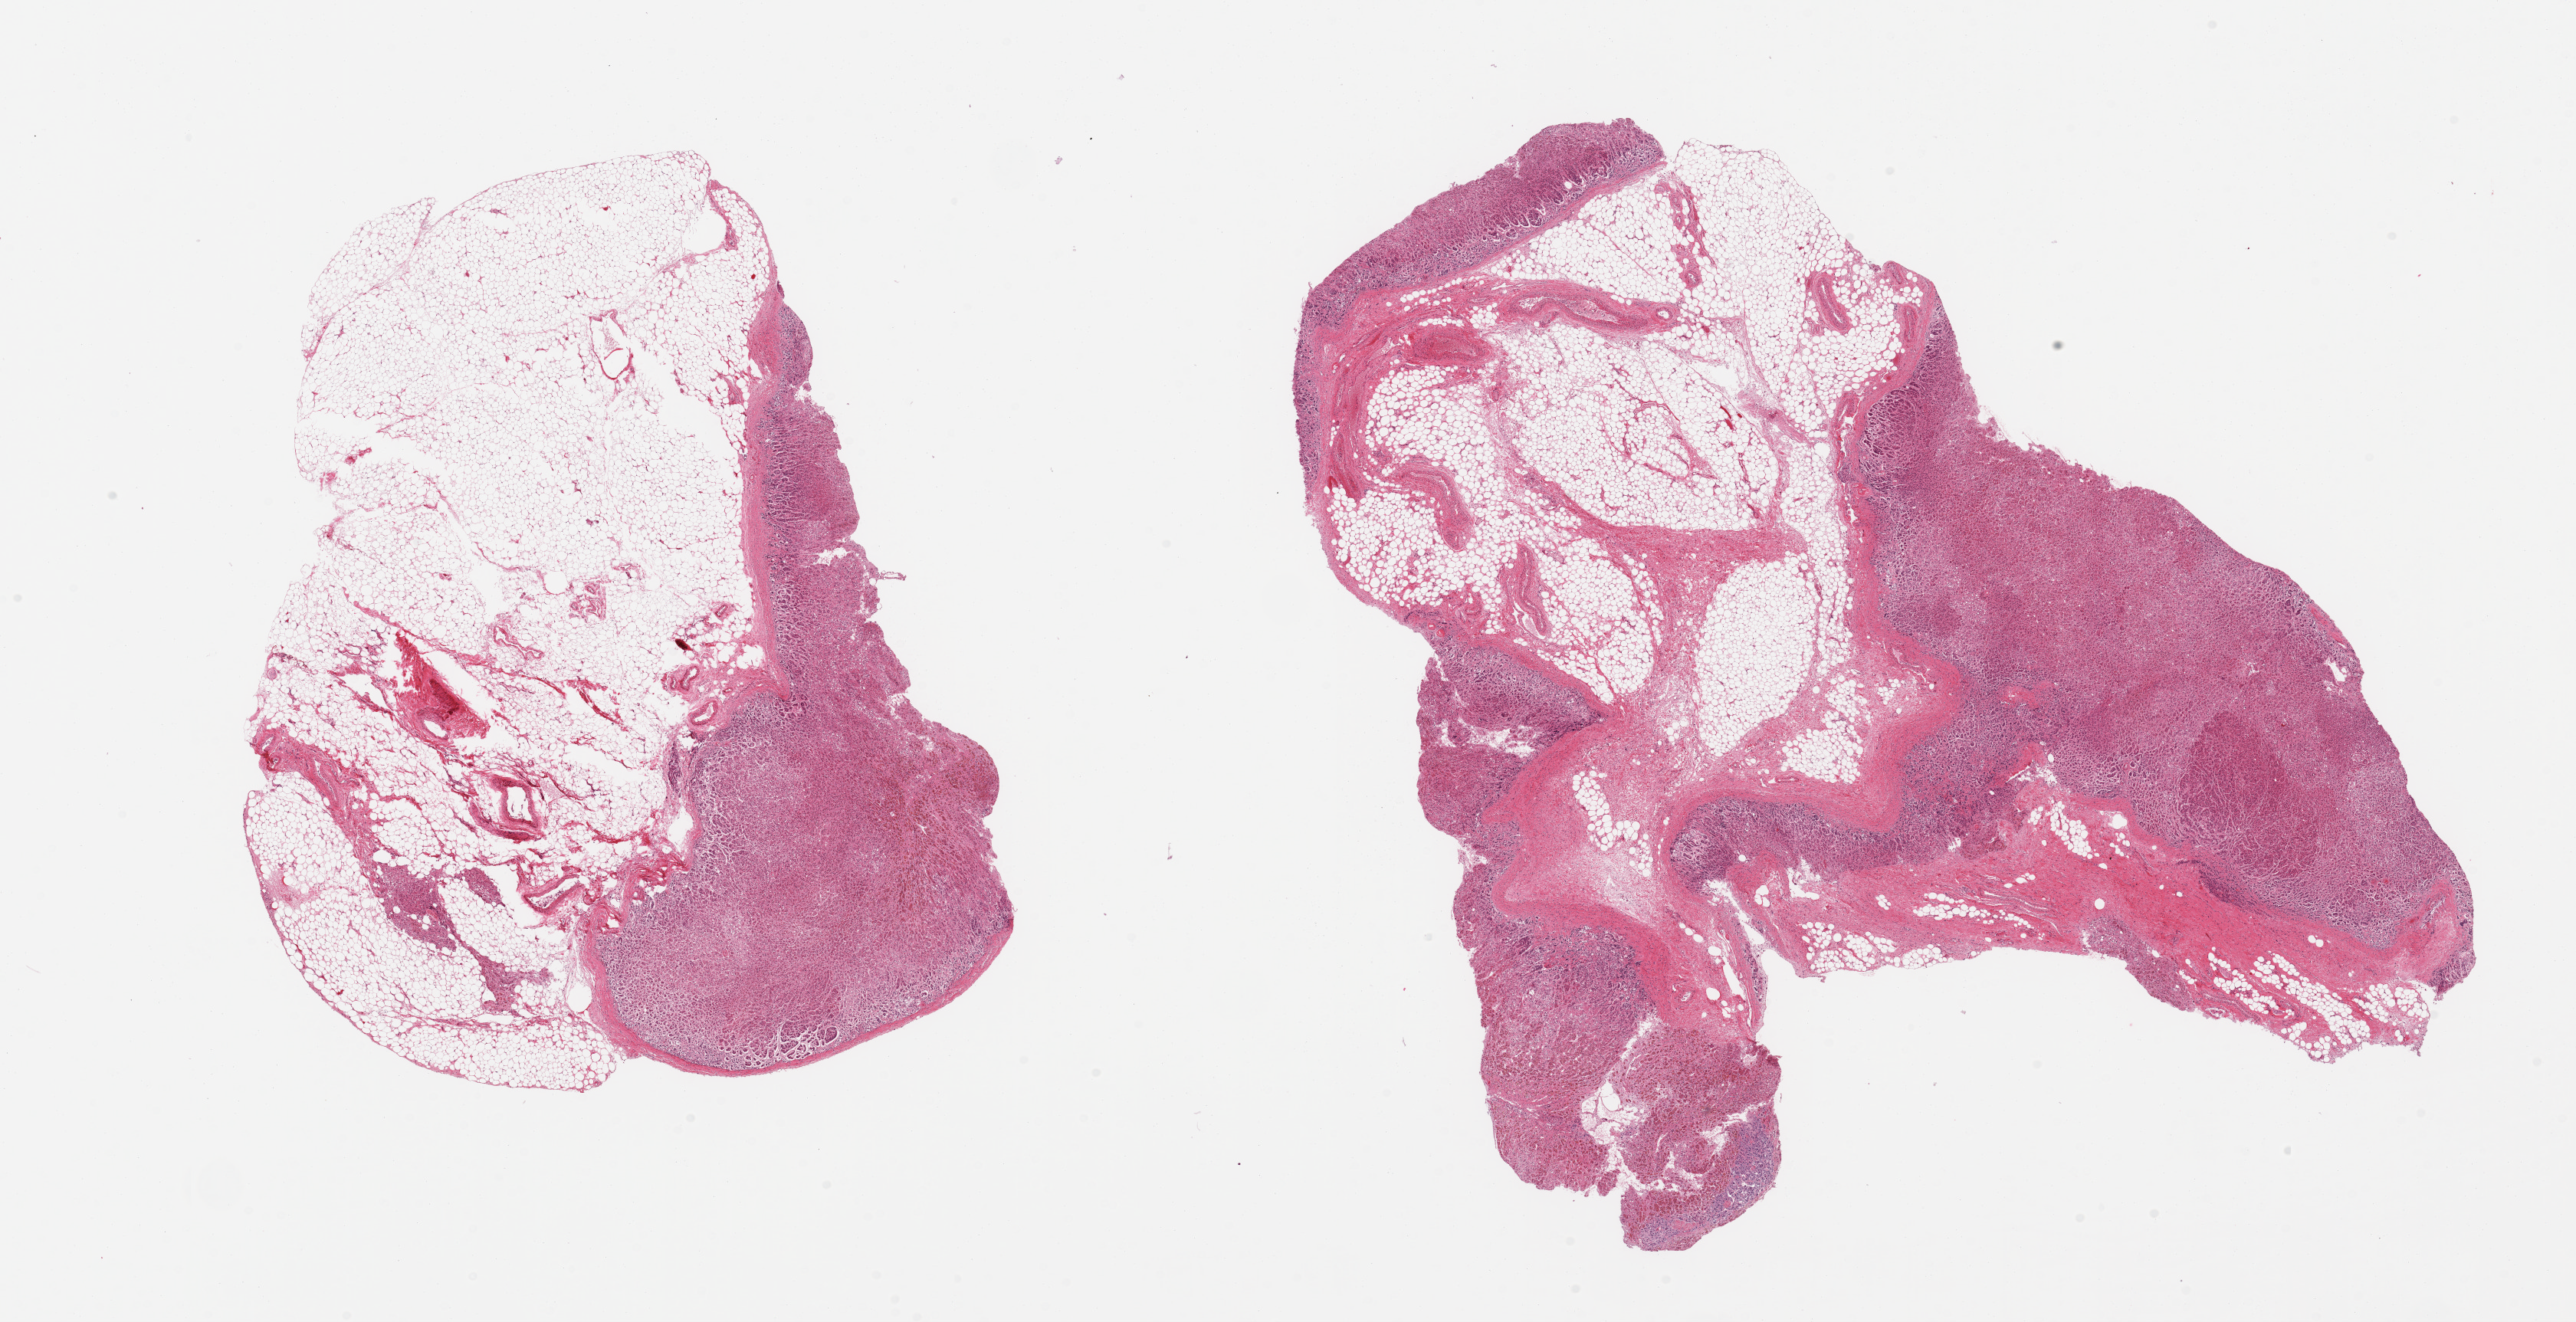
Whole-slide image, hematoxylin and eosin (H&E) stain, shown as a low-resolution overview of the whole scanned area (about 26.6 x 13.6 mm, acquisition: 20x scan), PAXgene-fixed paraffin-embedded (PFPE) section, section of adrenal gland (target tissue), tissue donor sample. Donor sex: male.
Pathologist's review note for this sample: 2 pieces, ~50% cortex; rest adherent/interstitial fat, autolyzed.